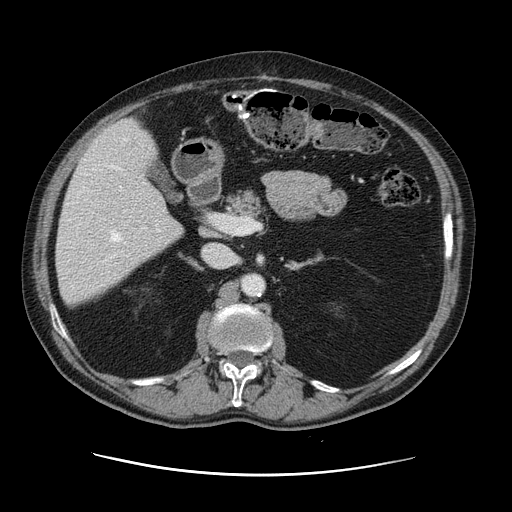
Contrast-enhanced abdominal CT, one axial slice; position 65 of 141 along the scan axis; soft-tissue window (W 400 / L 40 HU); 512 × 512 image matrix, field of view 395 × 395 mm. Male patient, age 72 years. From the clinical record (not read from this slice): diagnosis: colorectal cancer liver metastases, imaged before liver resection; multiple liver metastases: yes; largest metastasis: 5.4 cm; disease in both lobes: yes.
Annotated regions visible in this slice (expert manual segmentation):
- hepatic veins: bounding box (x1, y1, x2, y2) in pixels: (107, 138, 145, 257)
- liver: (57, 119, 183, 305)
- planned liver remnant (the part of the liver to remain after resection): (57, 187, 183, 305)
- portal vein (with intrahepatic branches): (134, 227, 149, 239)